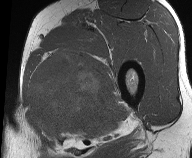
MRI of an extremity soft-tissue mass, one axial slice. Position 36 of 61 along the scan axis. MR volume resampled by the dataset authors to the PET/CT grid (not the native acquisition matrix). 3.27 mm slice thickness. 192 × 158 image matrix. Male patient. Case-level facts recorded for this patient, not image findings: histological type: pleiomorphic liposarcoma; grade: high; site of the primary tumour: left thigh.
Structures marked on this image (expert contour drawn on MRI and transferred to this co-registered scan by the dataset authors):
- gross tumour volume including surrounding oedema: bounding box <27,48,113,141> (left, top, right, bottom; pixels)
- gross tumour volume (mass): <29,50,112,129>